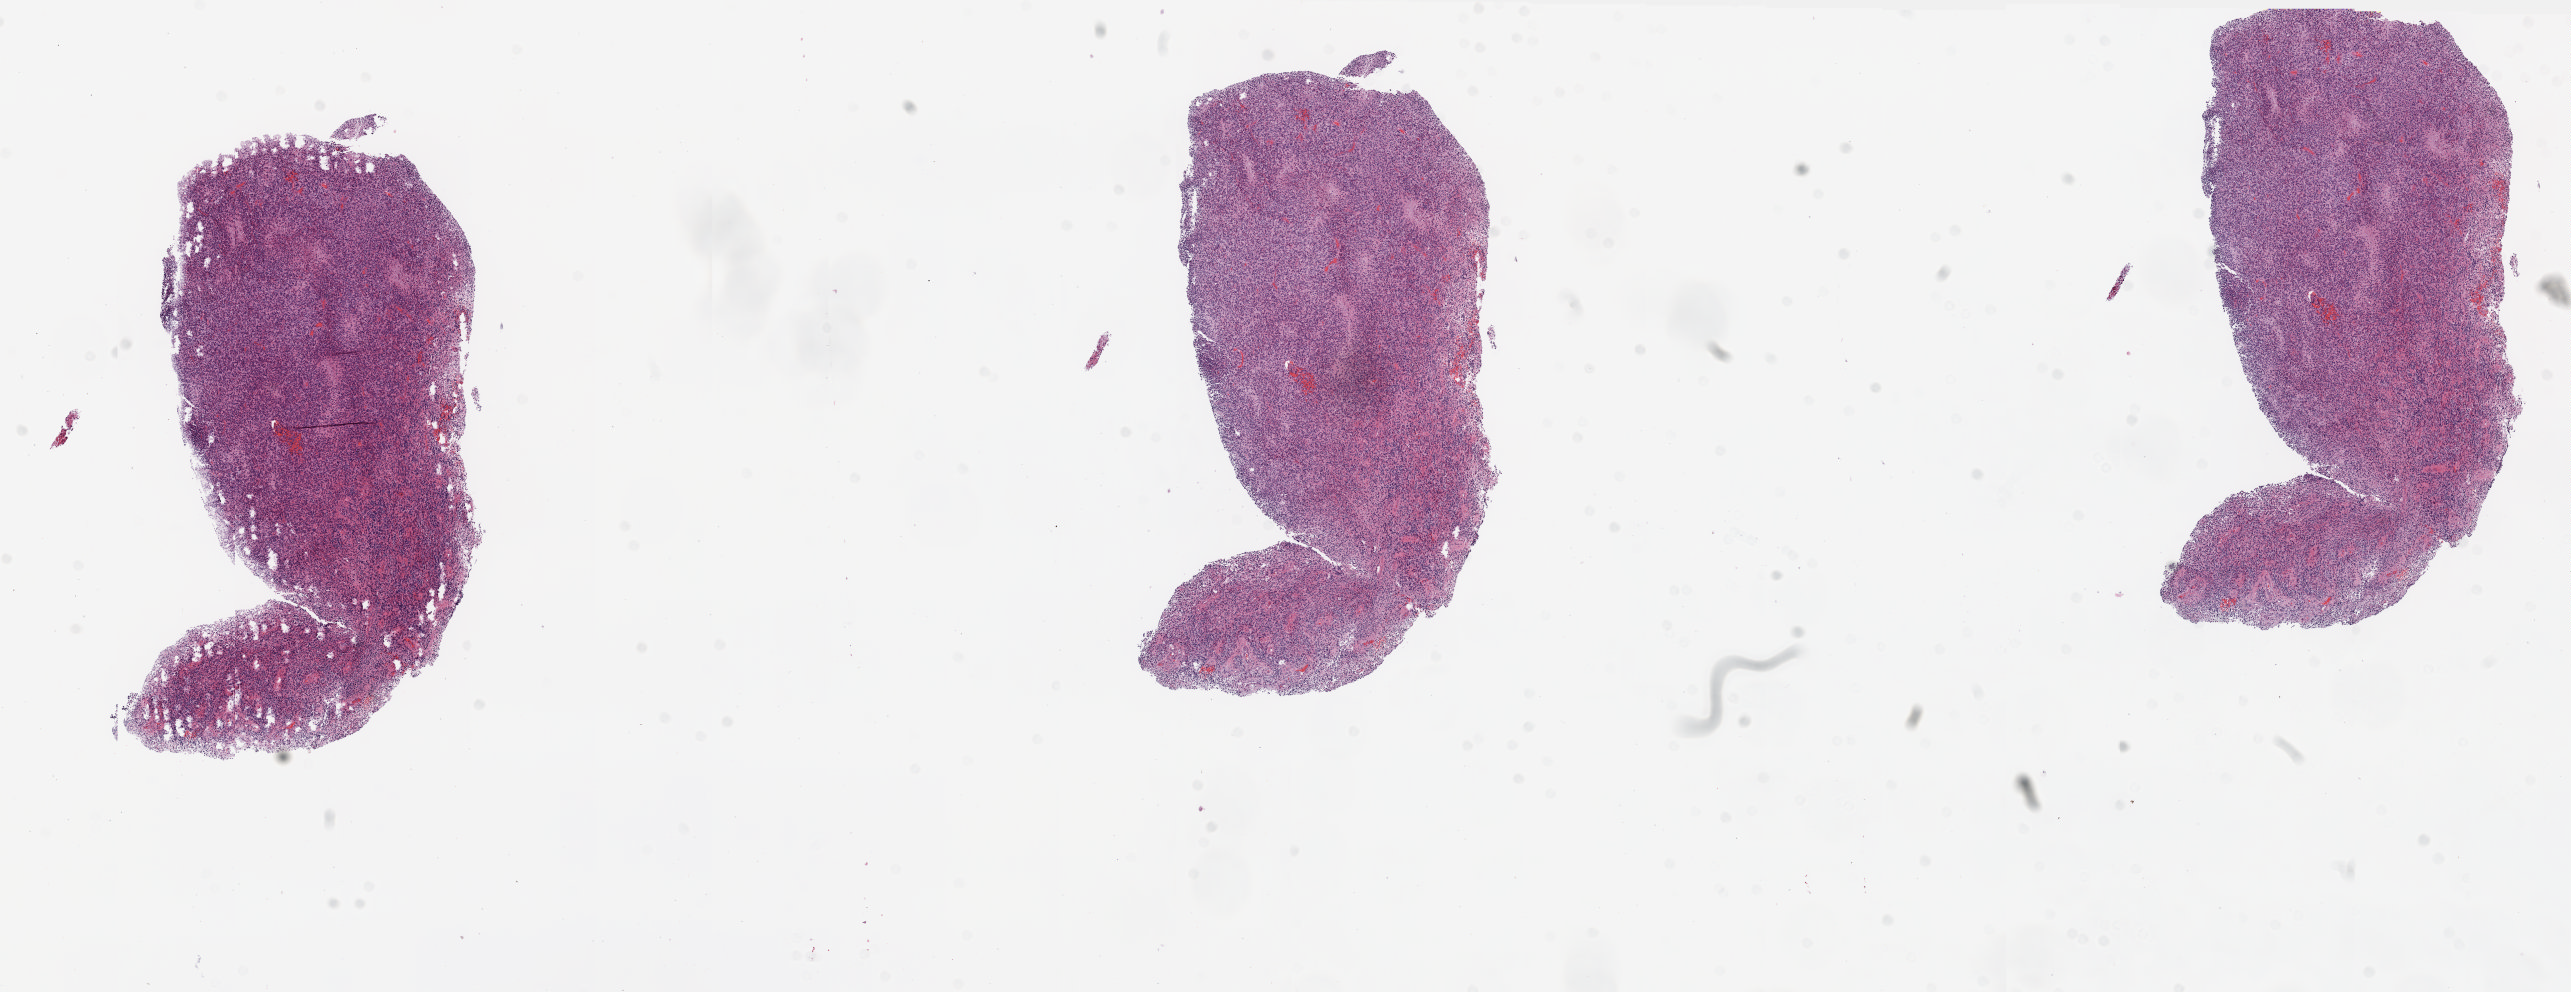
Whole-slide histology image, H&E-stained, shown as a low-resolution overview of the whole scanned area (about 20.6 x 8.0 mm). Frozen section. Brain, primary tumour sample. Female, age 54 years at initial diagnosis. Pathologist review of this section (percent, as recorded): tumour cells 90%, tumour nuclei 85%, normal cells 0%, stromal cells 0%, necrosis 10%.
• pathologic diagnosis: Glioblastoma